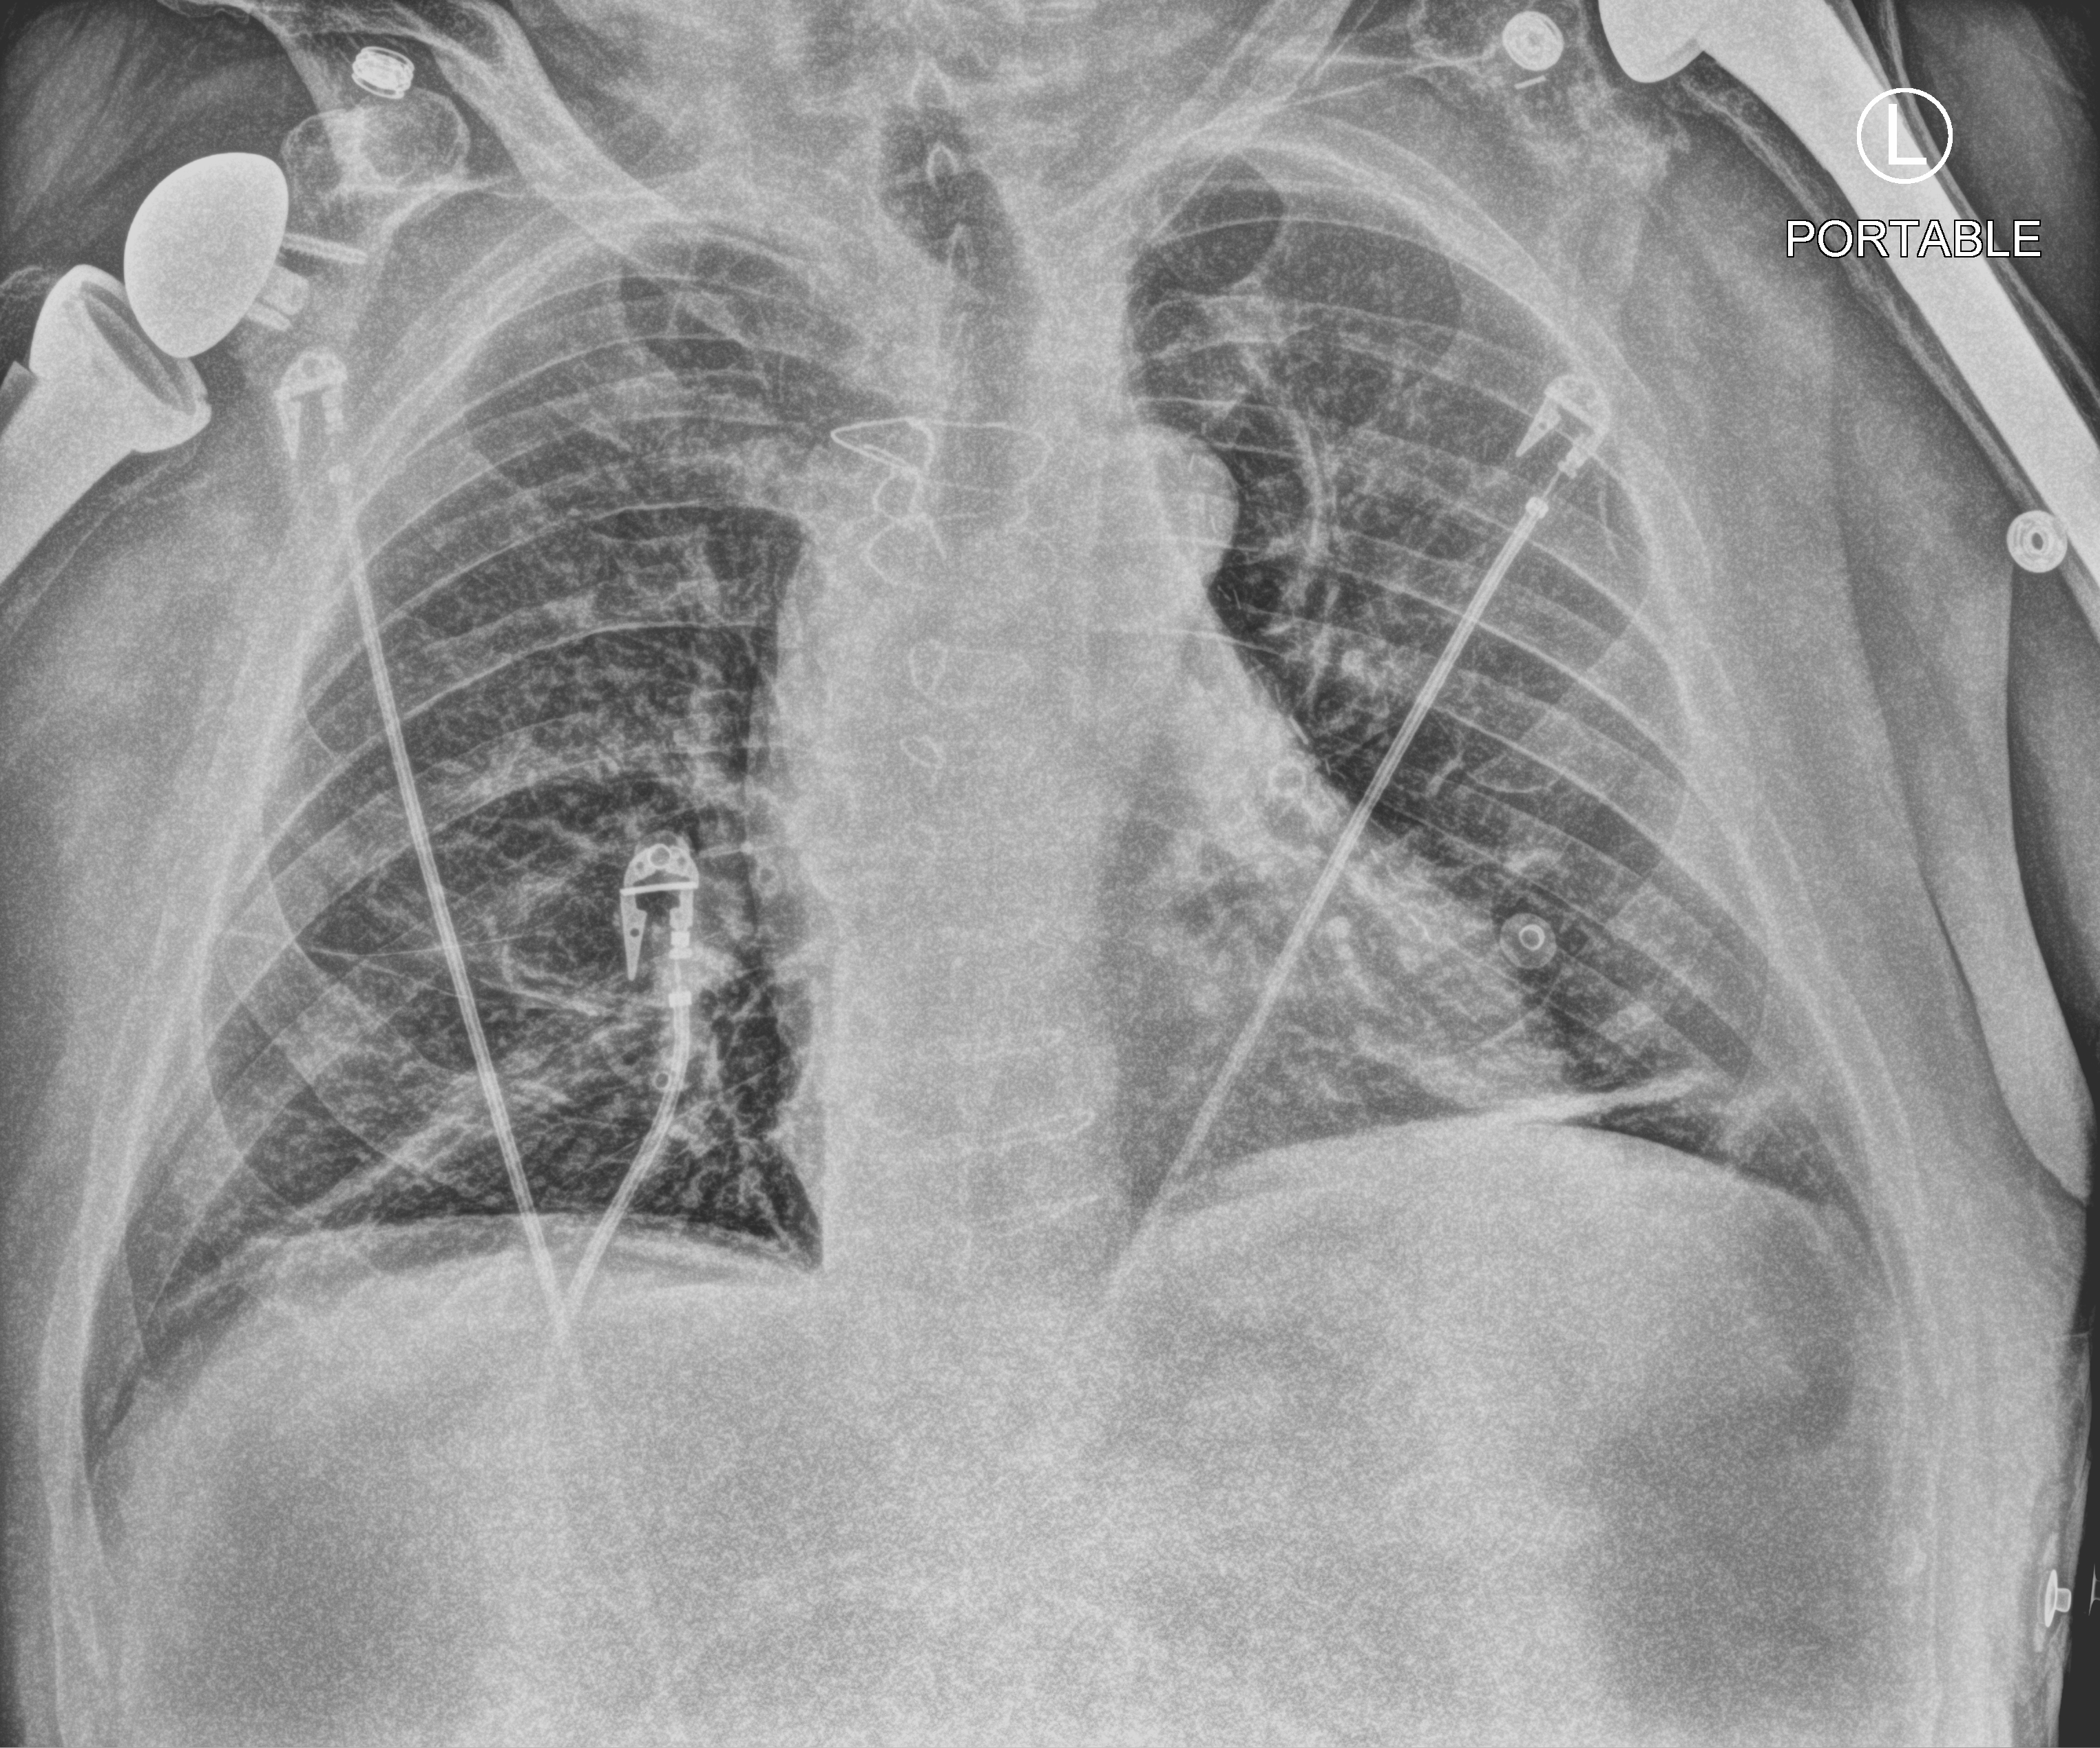
Bedside chest radiograph (computed radiography), anteroposterior (AP) projection. Patient hospitalised with COVID-19; male, aged 60–74 years.
Hospital-stay facts (about this admission, not read from this image; timing relative to this image not recorded): mechanically ventilated during this hospital stay: no; admitted to intensive care during this hospital stay: no; other chronic lung disease (admission record): no.